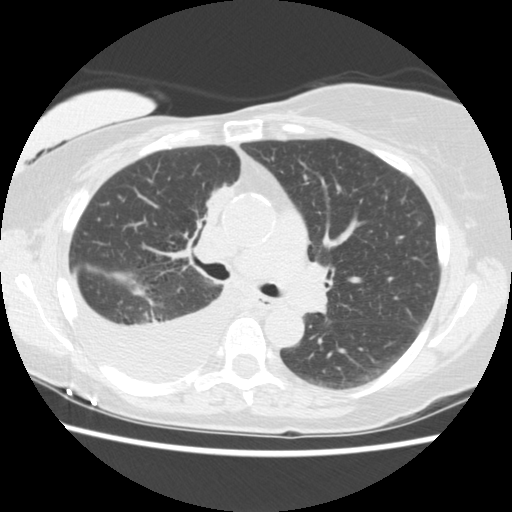
Axial slice from a low-dose chest CT screening exam, third screening round (two years after baseline), lung window (W 1500 / L -600 HU), standard (soft-tissue) reconstruction kernel (STANDARD), 120 kVp, slice 66 of 157 in the series. Female participant, aged 56 years at enrolment. Current smoker at enrolment.
• Expert reader's lesion annotation, bounding box [x1, y1, x2, y2] px = [183, 177, 246, 244].
• The screening reader recorded 2 non-calcified nodules or masses ≥4 mm on this exam; which of them this box marks is not recorded.